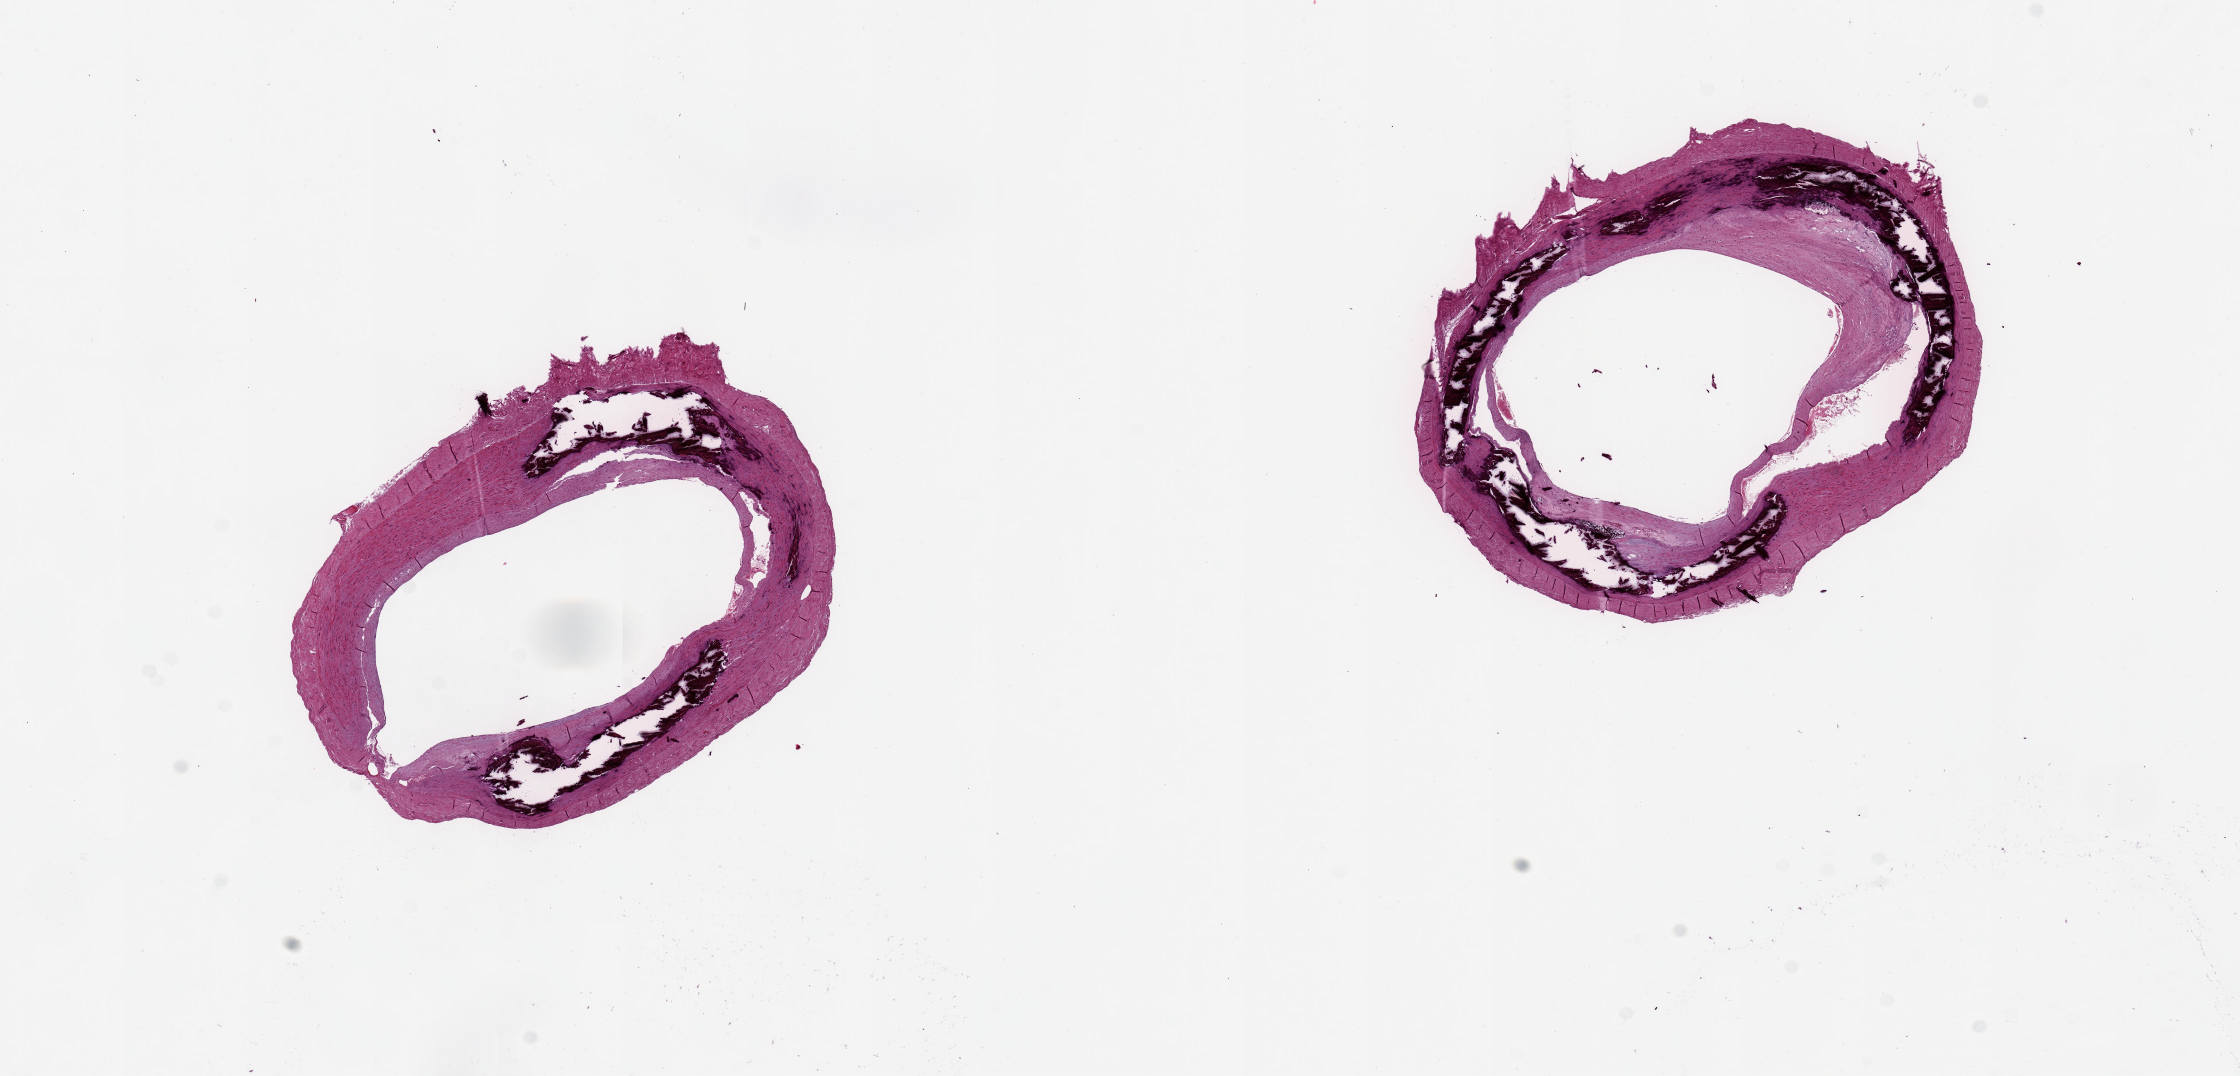
Hematoxylin and eosin (H&E) whole-slide image, brightfield — whole scanned area (about 17.7 x 8.5 mm) shown as a low-resolution overview. PAXgene-fixed paraffin-embedded (PFPE) section. Sampled site (target tissue): tibial artery. Tissue donor sample. Donor: male.
Reviewer comment on this tissue sample: 2 pieces ~4mm d; Moderate peripheral occlusive atherosclerosis ~30% Monckeberg's medial sclerosis in both.